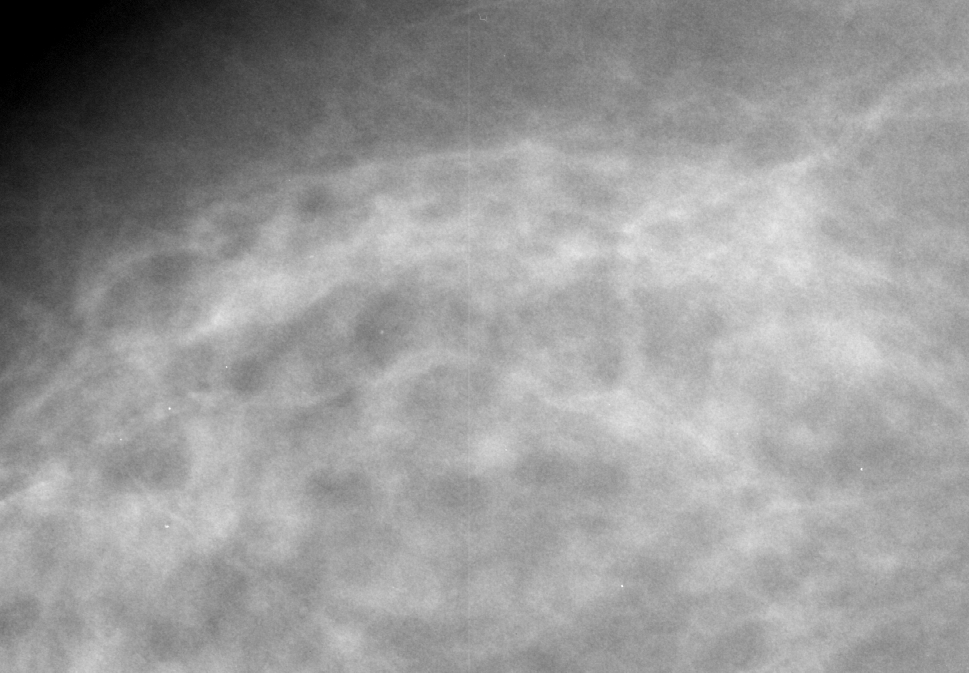
Cropped region of a digitized screen-film mammogram centred on a radiologist-marked abnormality; right breast; CC view; BI-RADS breast density category 3 (scale 1–4).
- Marked abnormality: calcifications, morphology vascular; BI-RADS assessment category 2; benign; no additional work-up was recommended (benign without callback).